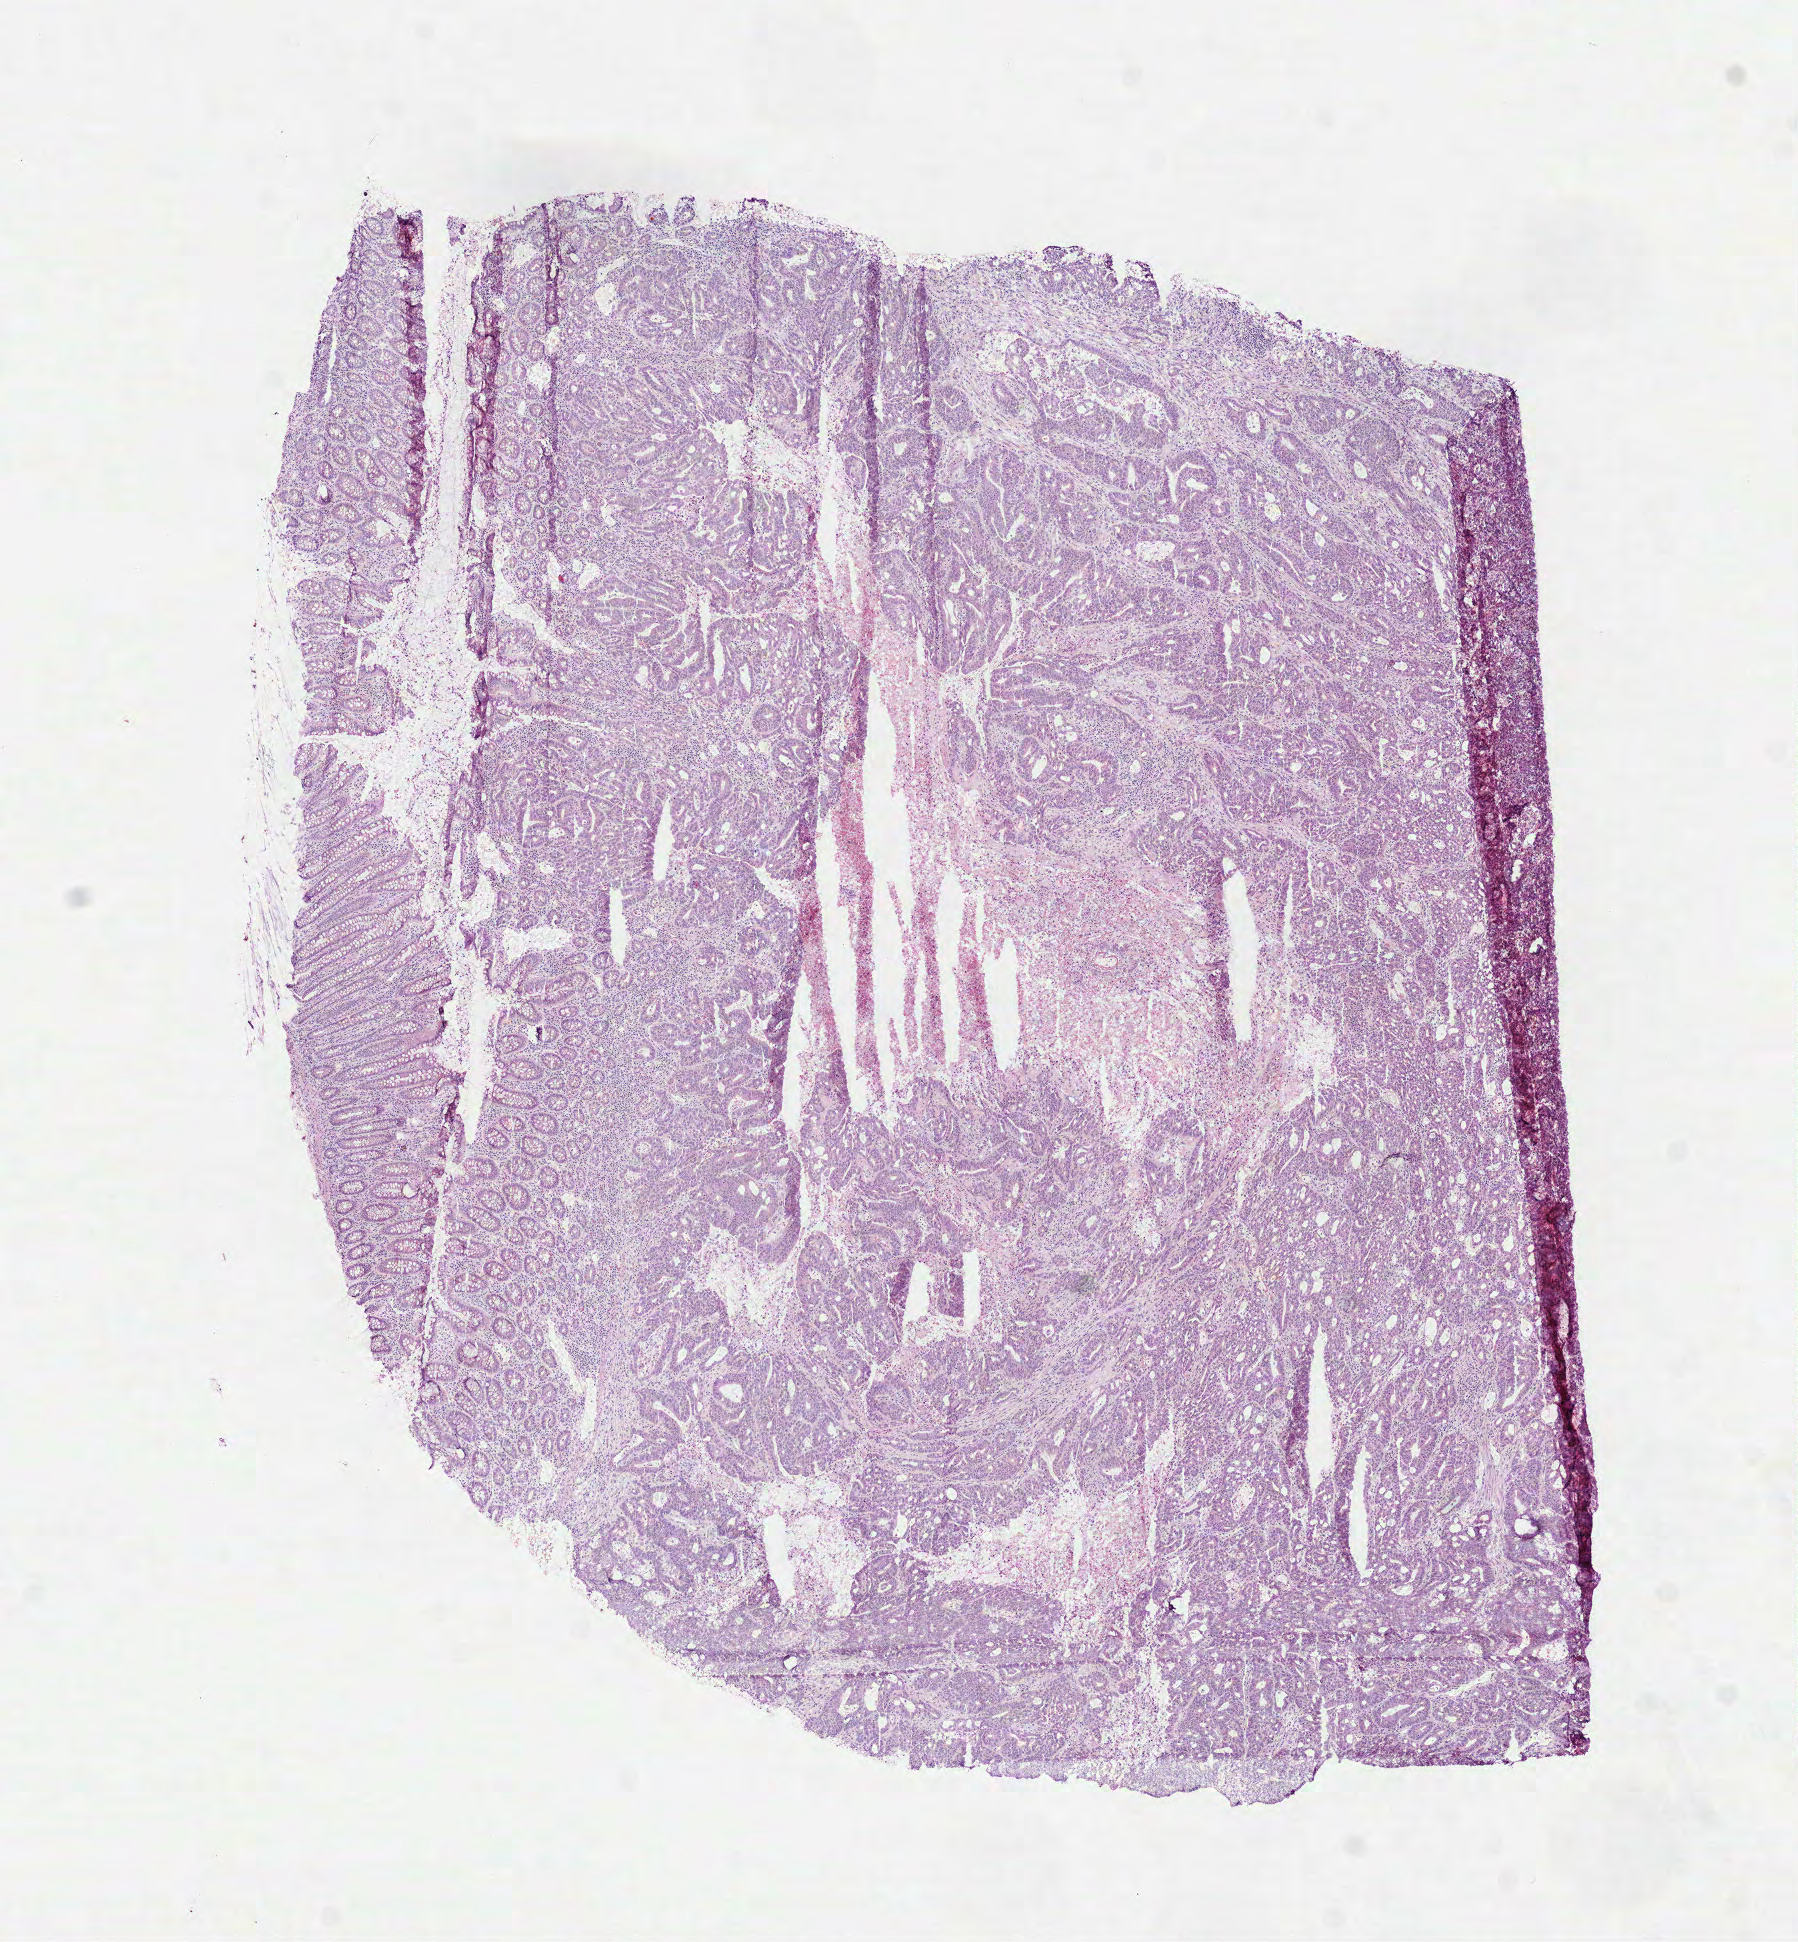
Whole-slide histology image, H&E-stained, whole scanned area (about 7.3 x 7.8 mm, from a 40x scan) shown as a low-resolution overview; frozen section; sample: primary tumour, colon. Male patient; age at initial diagnosis 77 years.
Pathologic diagnosis: Adenocarcinoma, NOS.